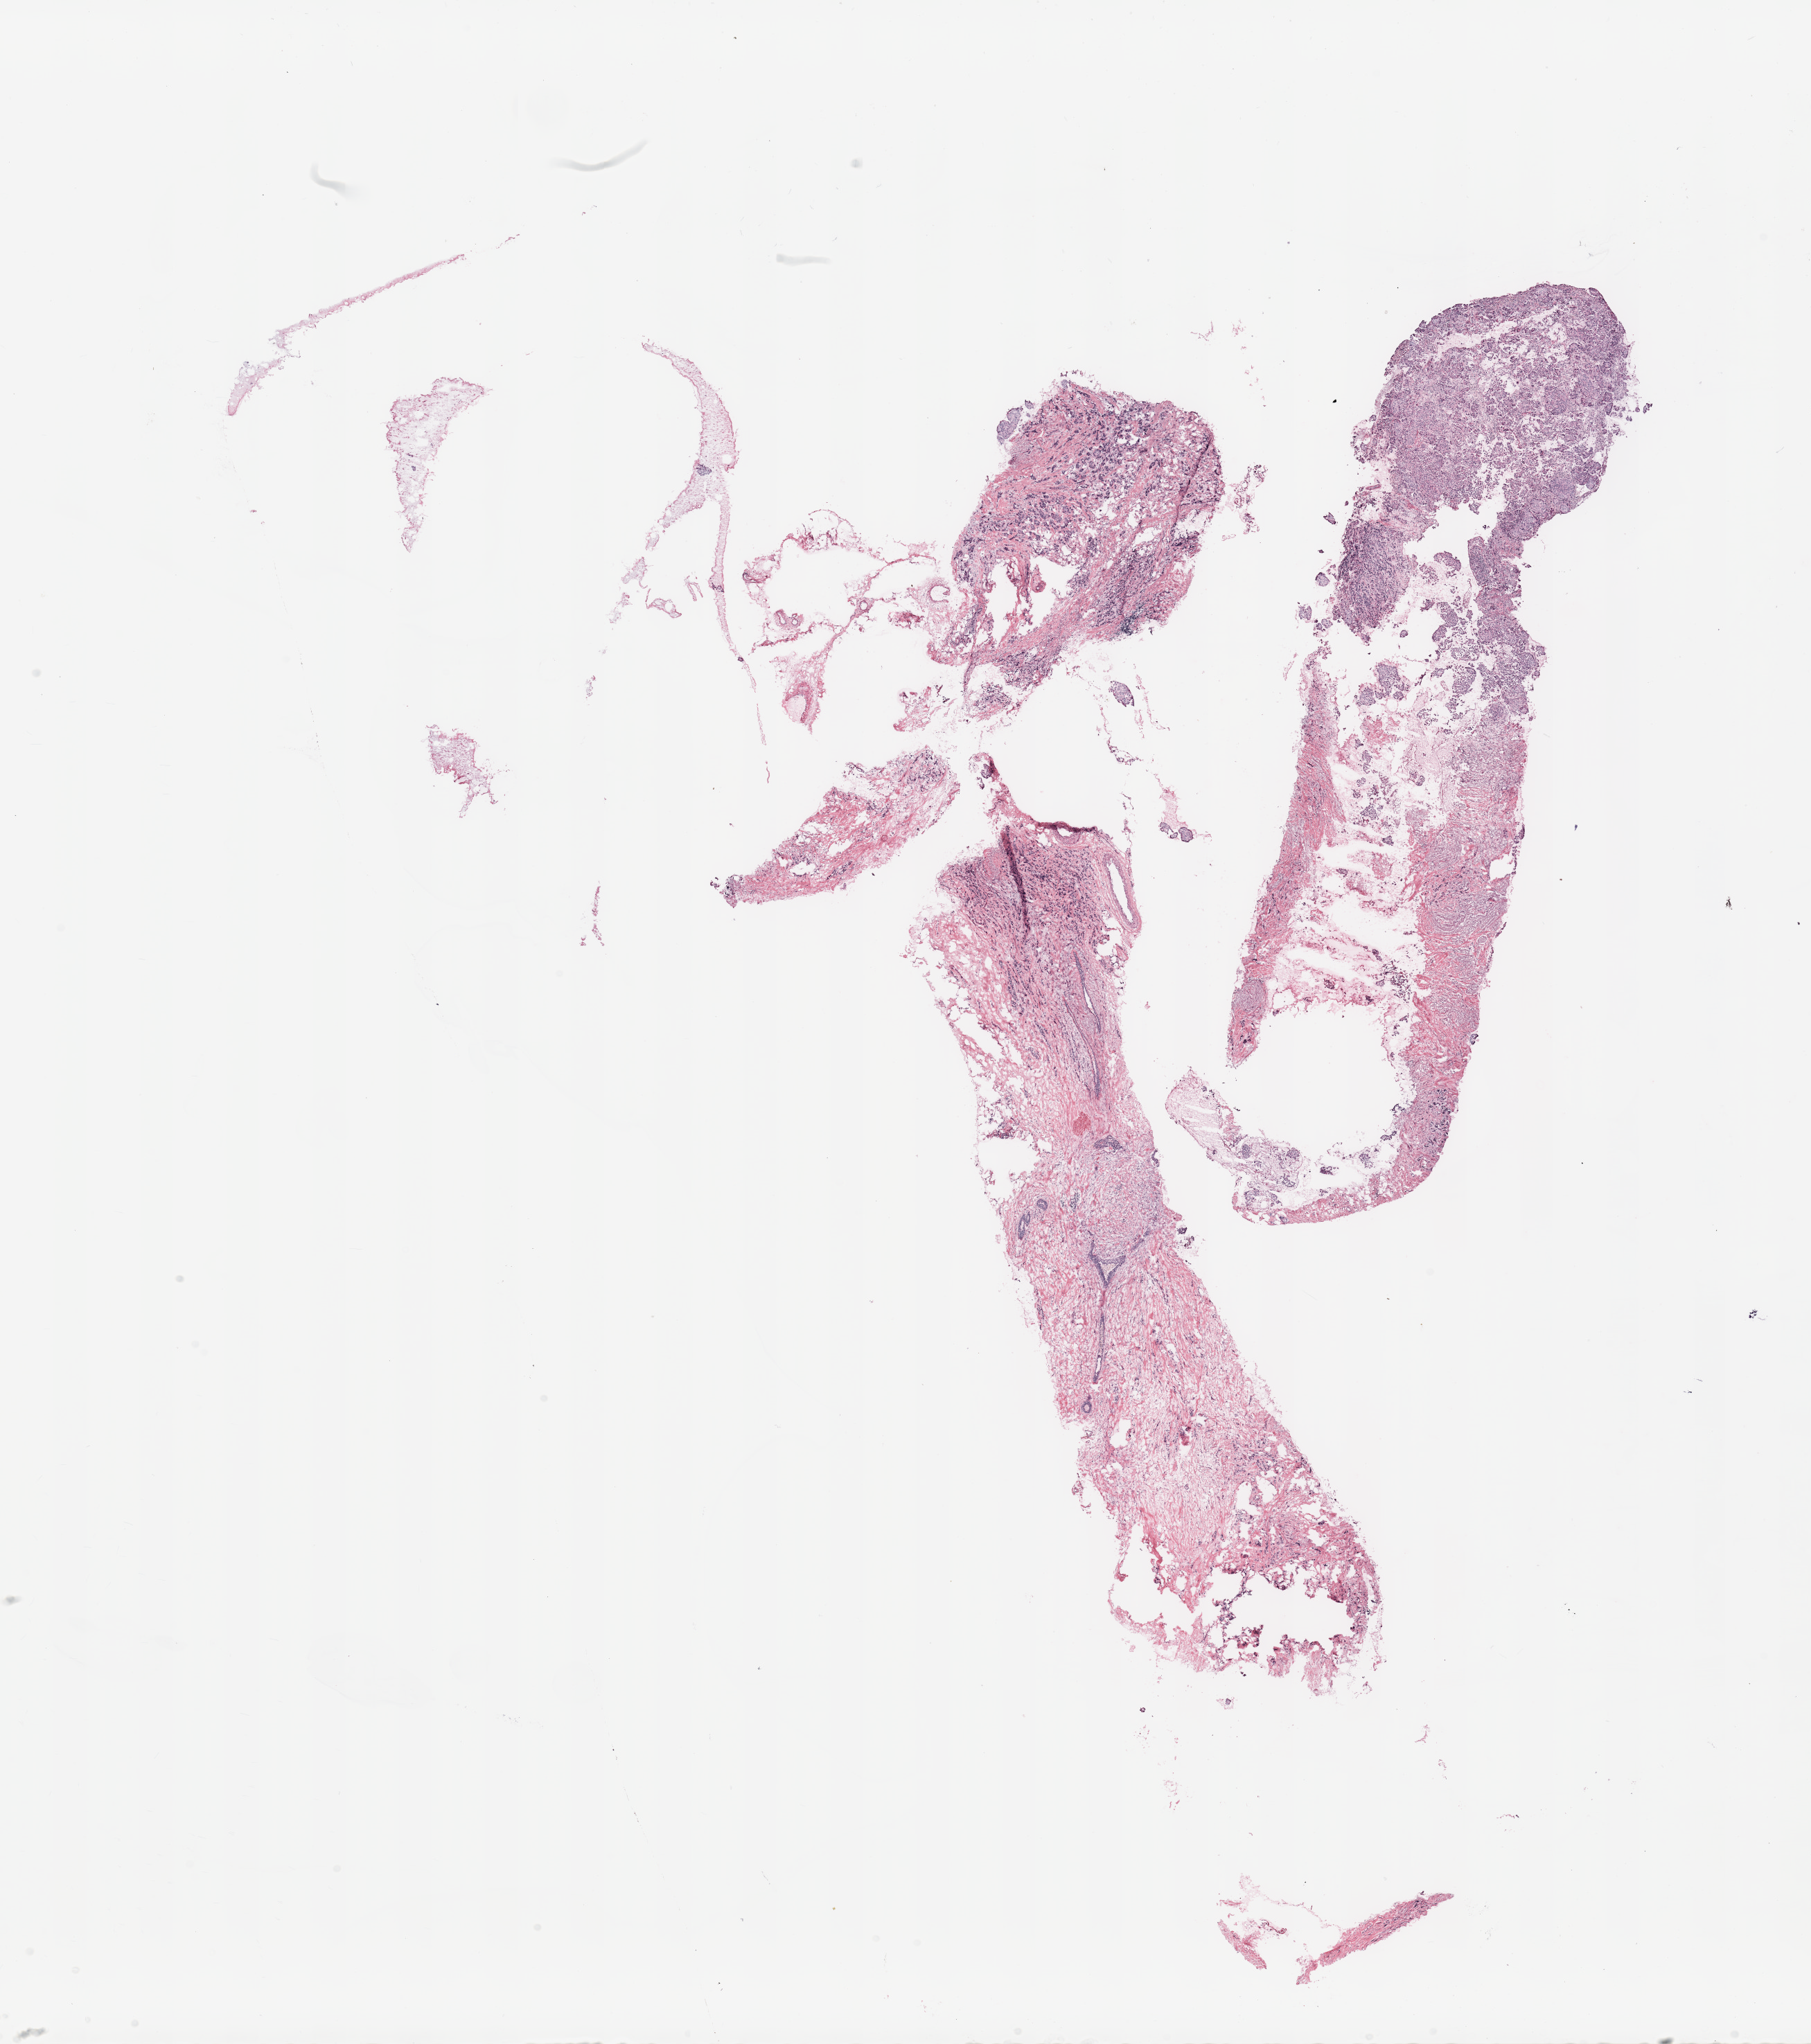
Whole-slide histology image, H&E, low-resolution overview of the scanned area, about 20.7 x 23.3 mm; tumour tissue sample, breast. 62-year-old female patient.
AJCC pathologic stage: IIIA. Histologic diagnosis: Infiltrating duct carcinoma, NOS.